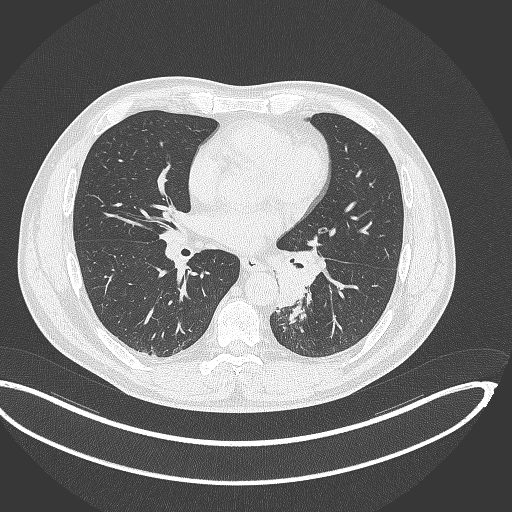
Chest CT, one axial slice. Position 170 of 362 along the scan axis. 120 kVp. Lung window (W 1500 / L -600 HU). 1 mm slice thickness. 512 × 512 image matrix, field of view 442 × 442 mm. Male patient, age 50 years. Case-level facts recorded for this patient, not image findings: clinical TNM (as recorded): T2a N3 M0.
Outlined on this slice (rectangle marked by the reading radiologist):
- lung tumour (recorded histology: squamous cell carcinoma): box from (x=271, y=242) to (x=327, y=311) px